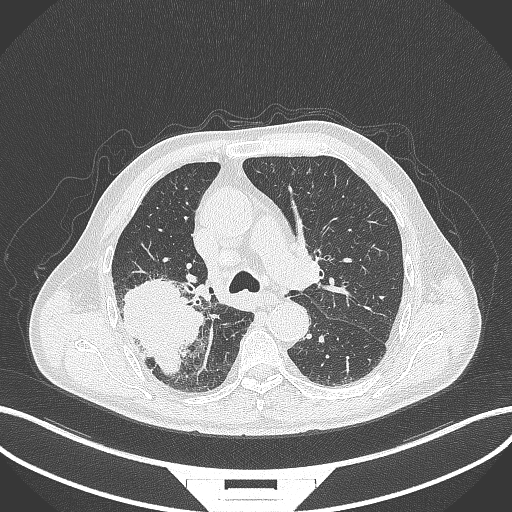
Chest CT, one axial slice; position 268 of 429 along the scan axis; 120 kVp; lung window (W 1500 / L -600 HU); 1 mm slice thickness; 512 × 512 image matrix, field of view 400 × 400 mm. Patient: male, 72 years. From the clinical record (not read from this slice): clinical TNM (as recorded): T3 N2 M0.
Outlined on this slice (rectangle marked by the reading radiologist):
- lung tumour (recorded histology: adenocarcinoma): bounding box [x1, y1, x2, y2] px = [114, 274, 203, 379]